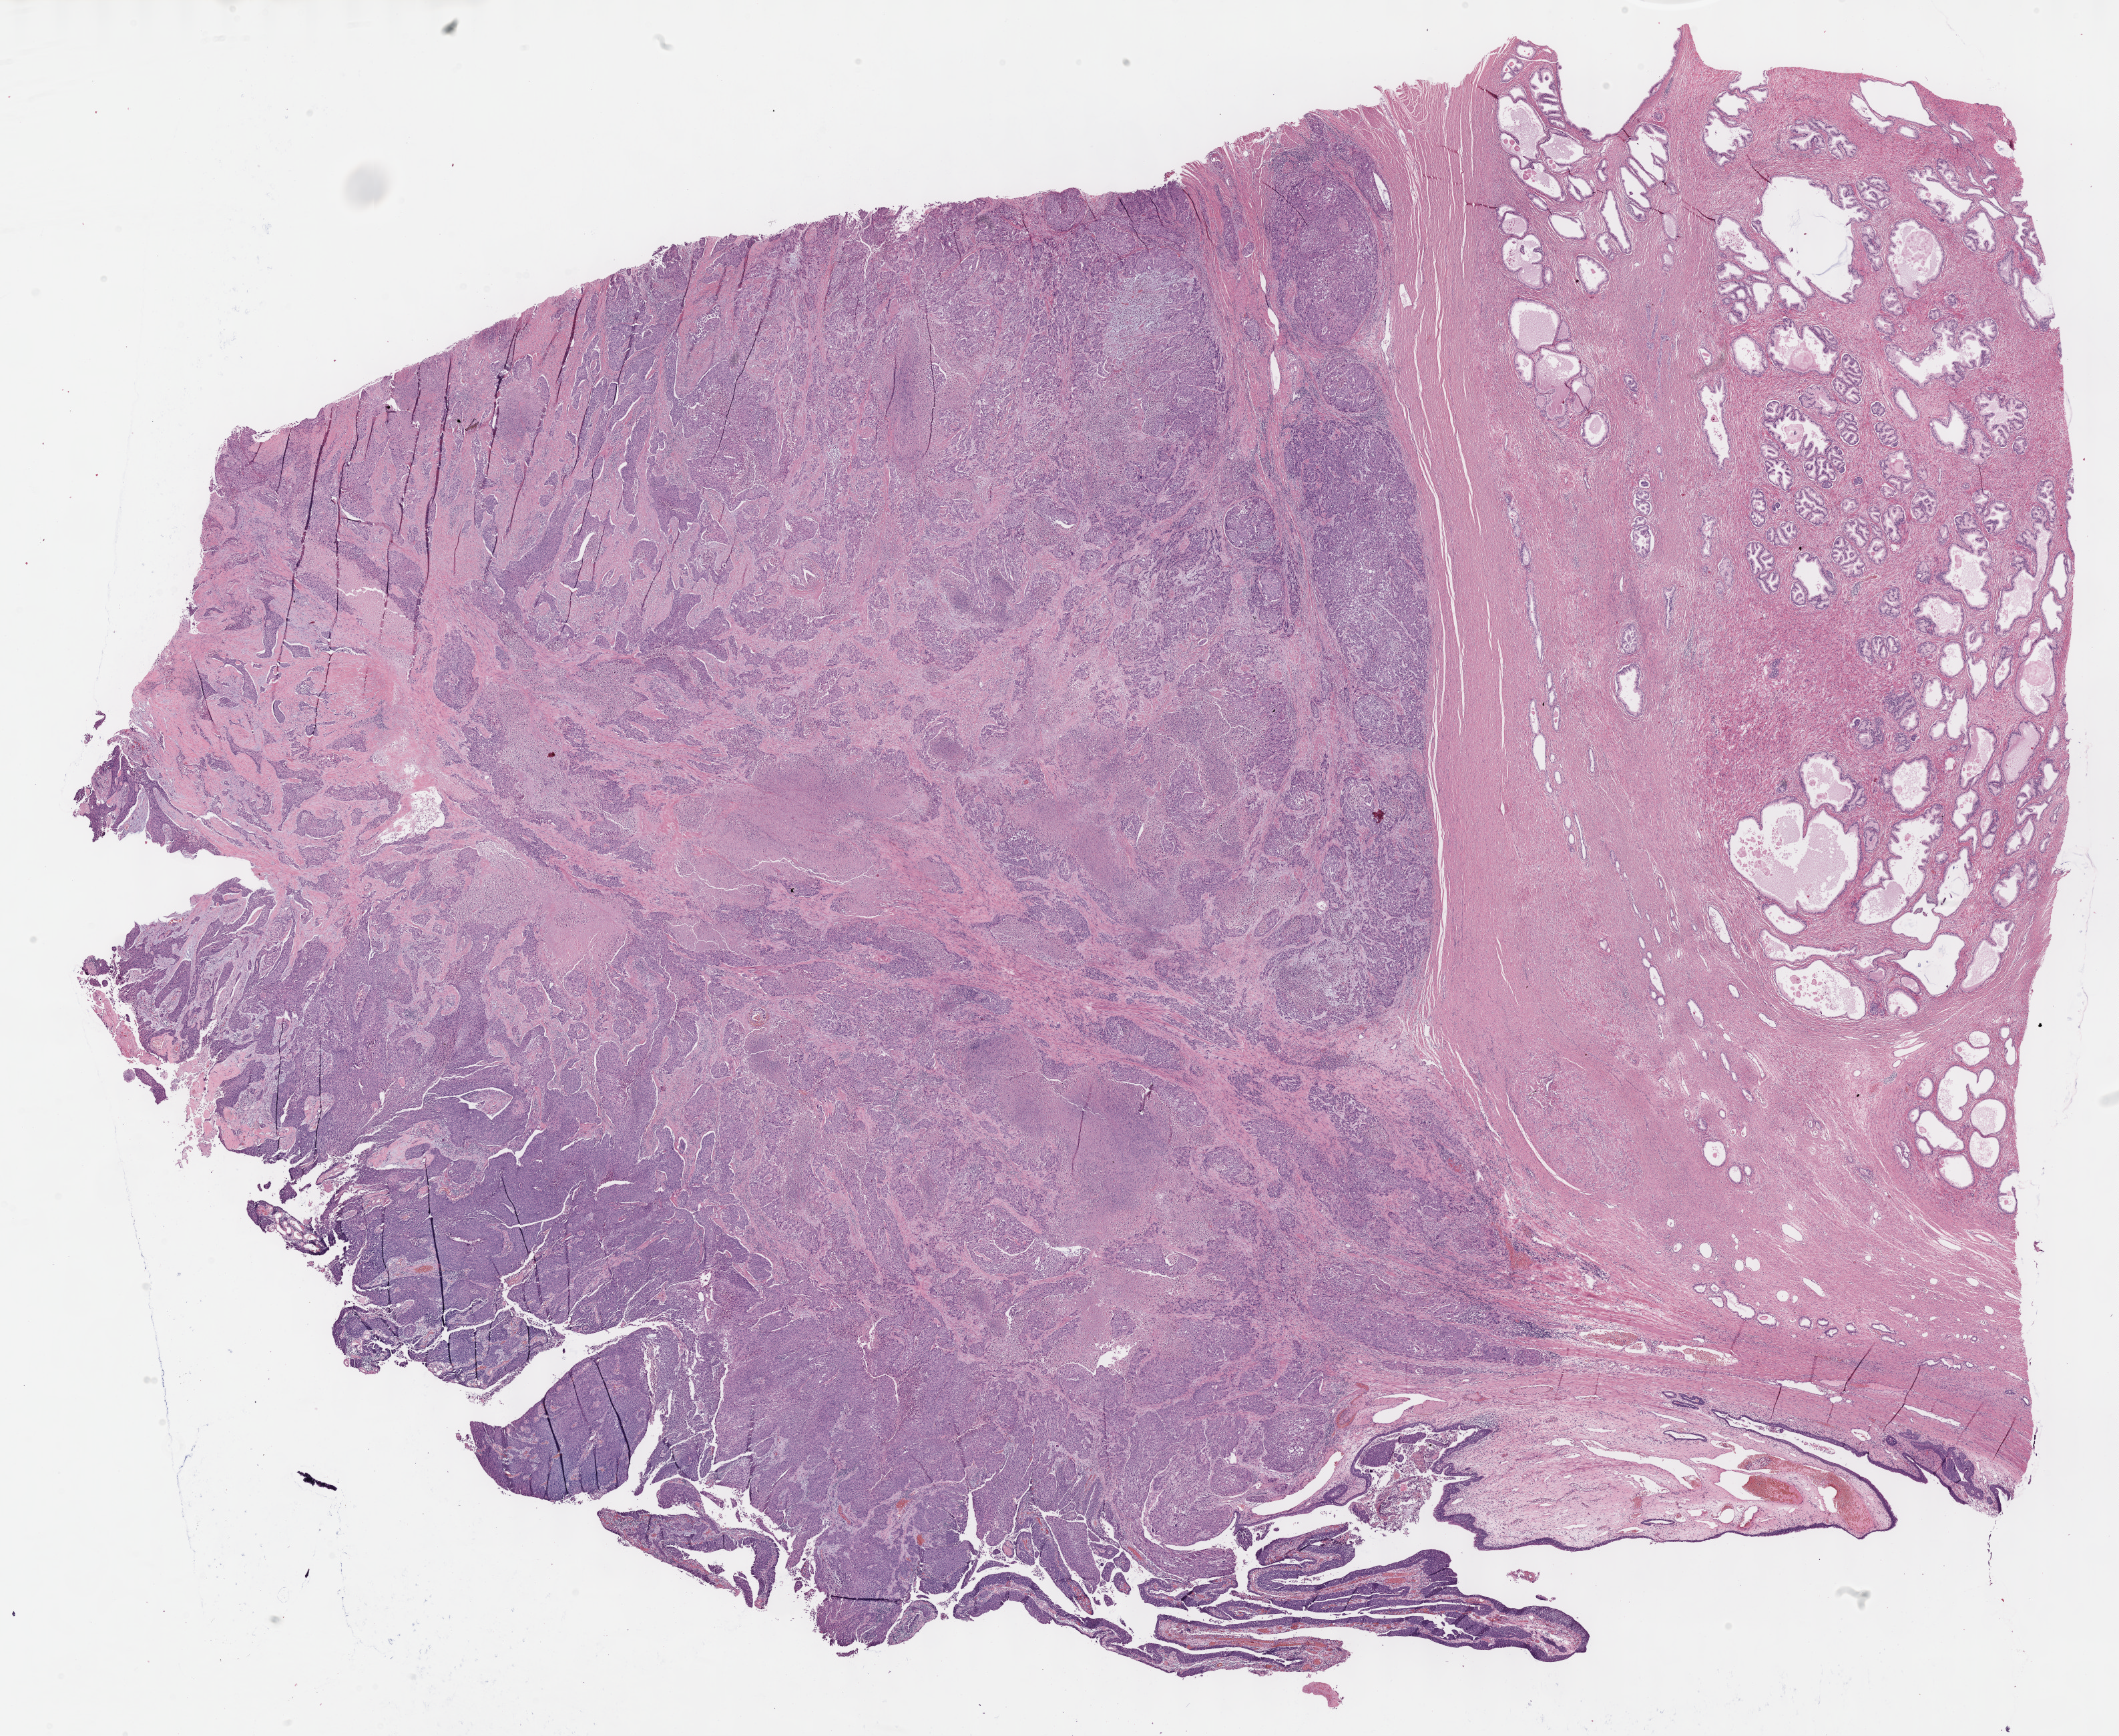
Whole-slide histology image, H&E-stained, shown as a low-resolution overview of the whole scanned area (about 25.7 x 21.0 mm, slide scanned at 40x); formalin-fixed paraffin-embedded (FFPE) diagnostic section; bladder, primary tumour sample. Patient: male, age at initial diagnosis 60 years. Histologic grade: high grade.
AJCC pathologic stage: IV. TNM: T4b N0 M0. Pathologic diagnosis: Papillary transitional cell carcinoma (trigone of bladder).